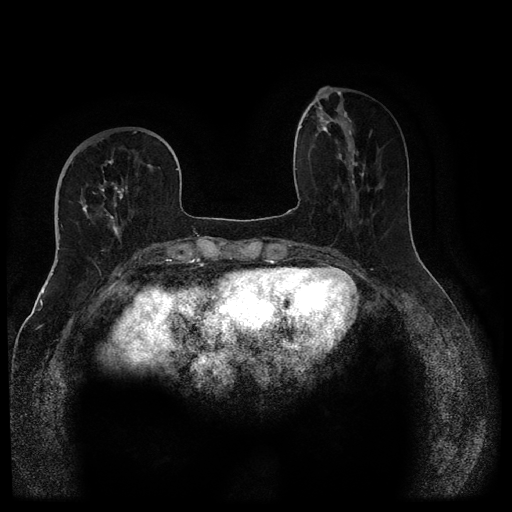
Breast MRI (dynamic contrast-enhanced, multi-phase), one axial slice; position 39 of 116 along the scan axis; dynamic contrast-enhanced series, time point 2 of 5 at this slice position (early post-contrast); 1.5 T; TE 2.6 ms, TR 5.4 ms; 2 mm slice thickness; 512 × 512 image matrix, field of view 340 × 340 mm. Patient: female, 68 years.
Structures marked on this image (semi-automatically segmented with operator editing):
- breast lesion (labelled benign in the annotation): bounding box (x1, y1, x2, y2) in pixels: (315, 108, 355, 144)